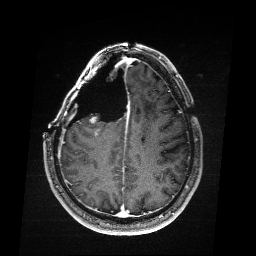
Brain MRI from a brain-tumour surgery series, one axial slice; slice 69 of 176 in the series (ordered by position); T1-weighted post-contrast; 256 × 256 image matrix, field of view 256 × 256 mm. Case-level facts recorded for this patient, not image findings: histopathology: Astrocytoma; WHO grade: 4; IDH mutation: yes; tumour location: Right Frontal.
Structures marked on this image (outlined manually by an expert reader):
- residual tumour: bounding box <106,117,116,136> (left, top, right, bottom; pixels)